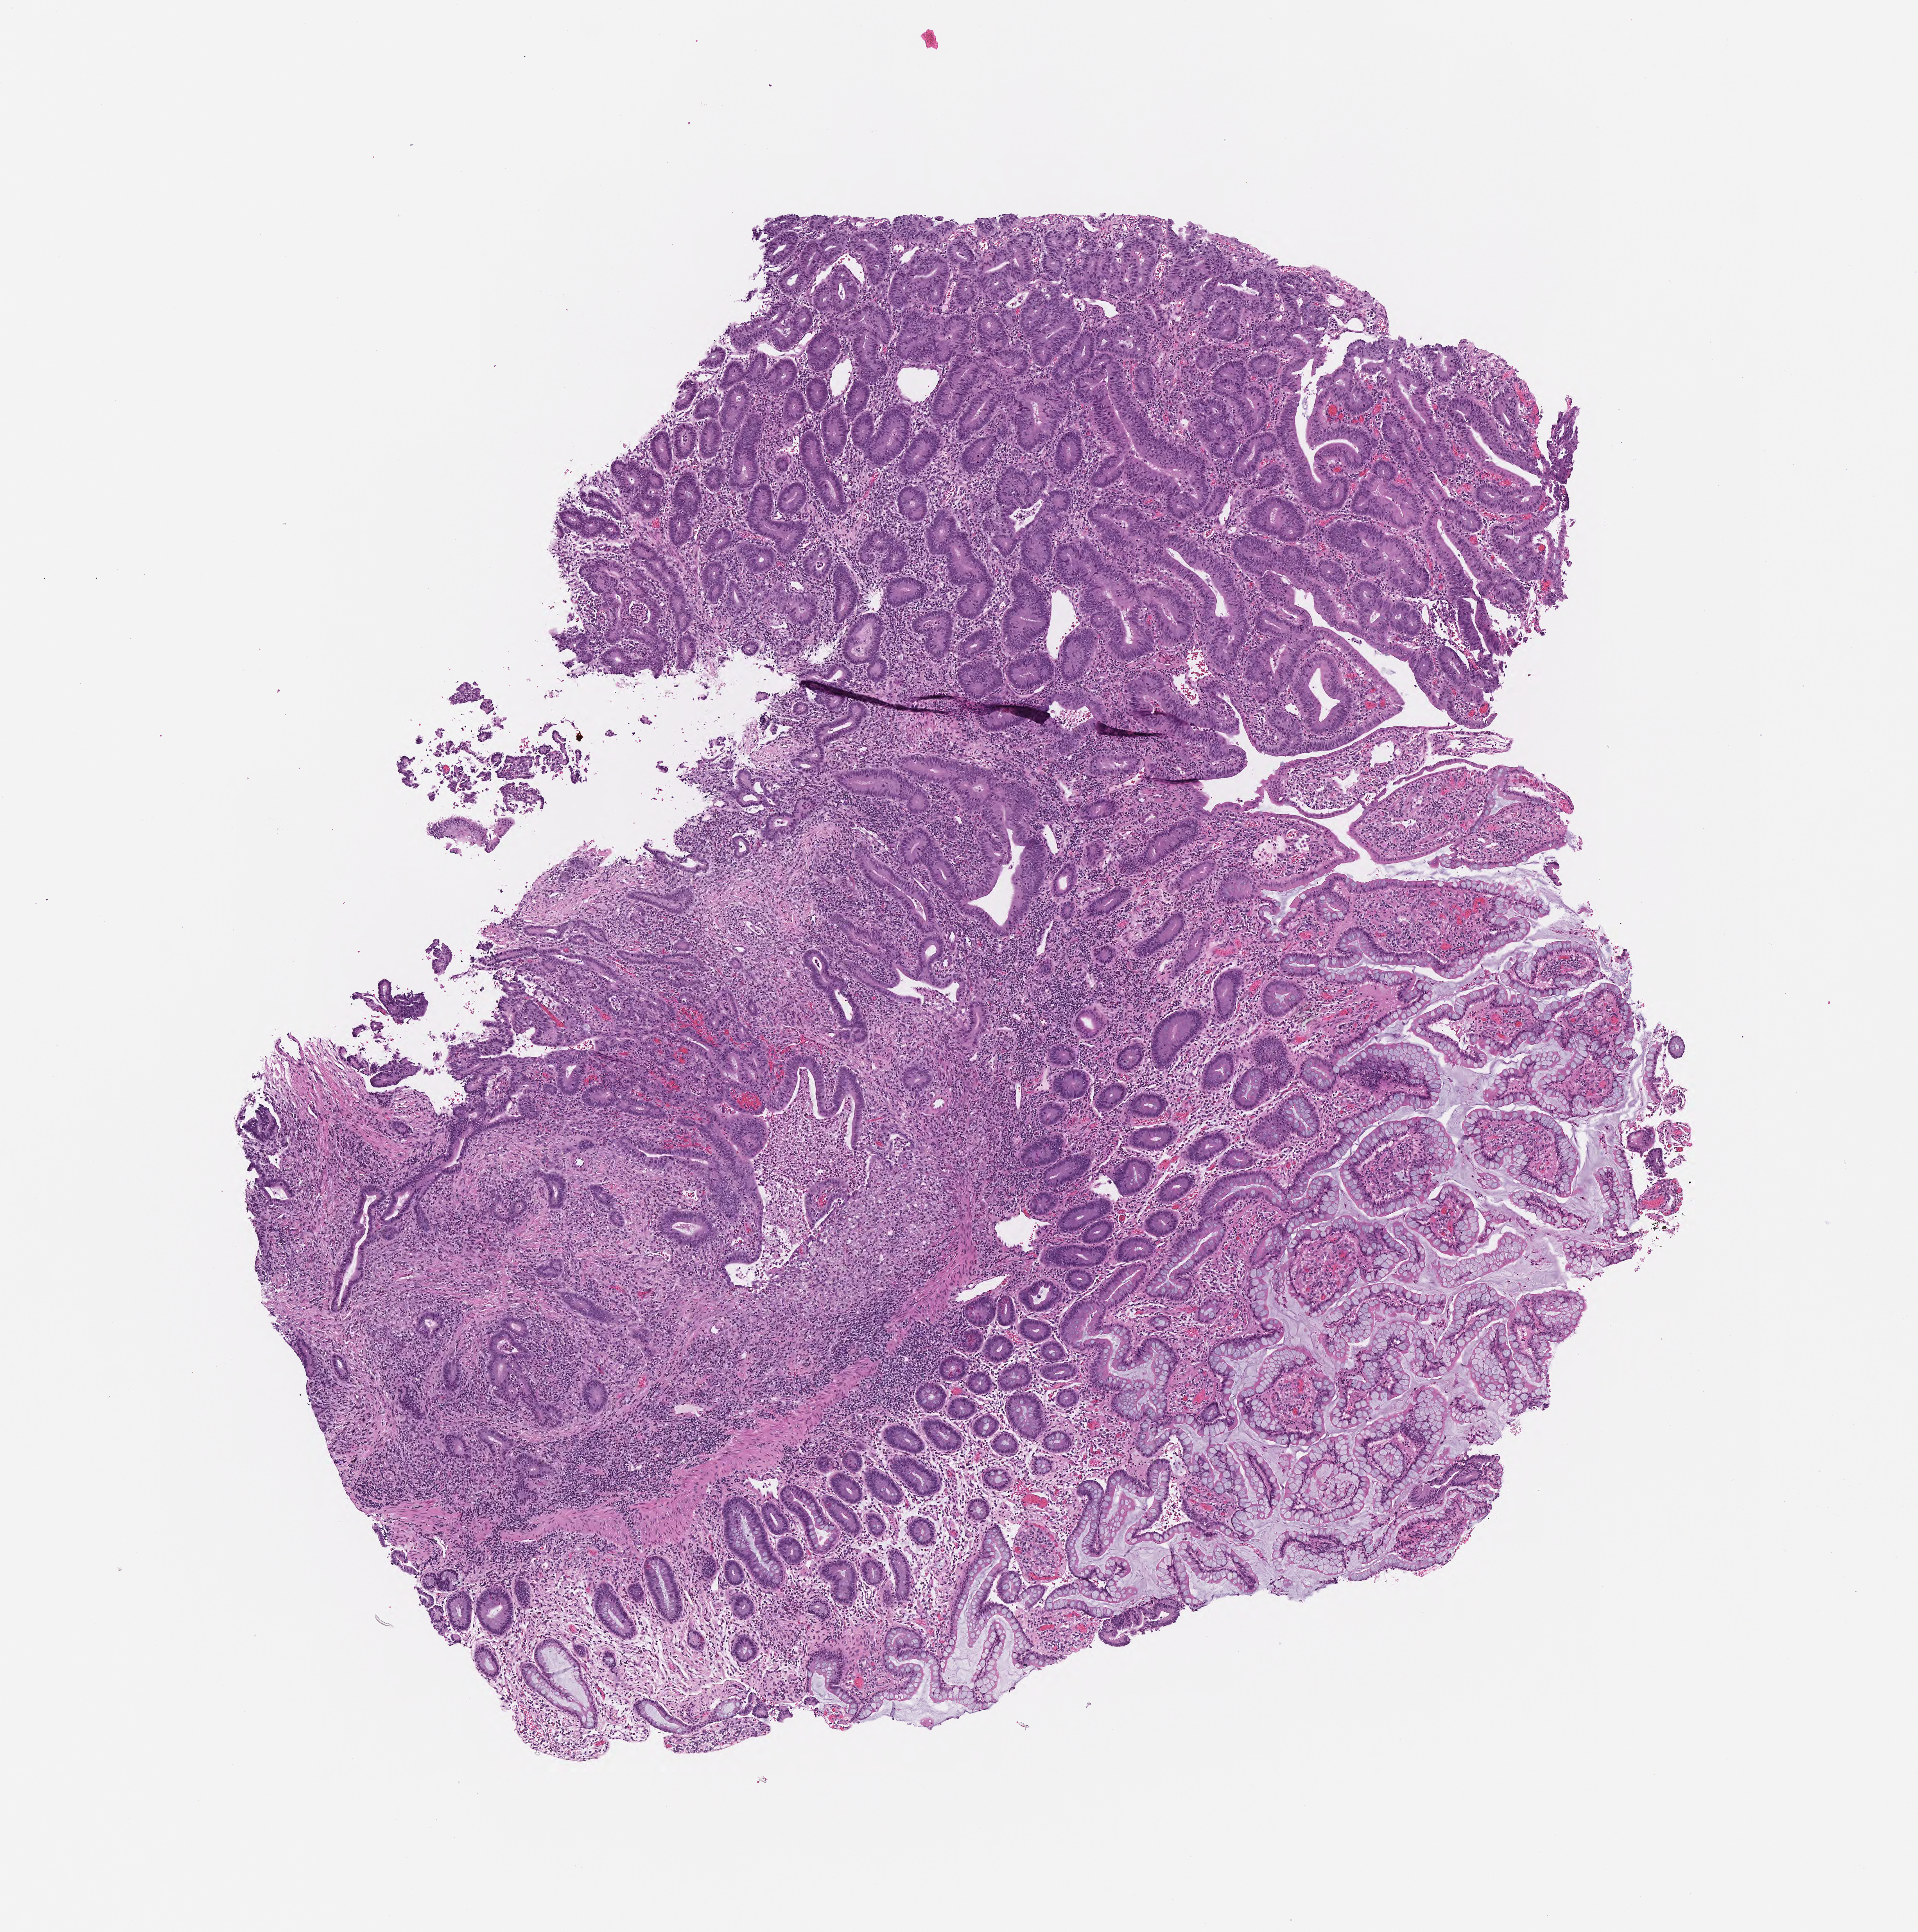
Digitized H&E-stained section — a low-resolution overview of the entire scanned area, about 6.0 x 6.1 mm; FFPE section; specimen: primary tumor; site: ileum. Male patient; age at initial diagnosis 57 years. Tumor grade: G2 (moderately differentiated). Slide review estimates, as recorded: tumor cells 65%, tumor nuclei 65%, stromal cells 28%, necrosis 2%, normal cells 5%. Infiltration values recorded for this section: lymphocyte infiltration 4%, monocyte infiltration 4%, neutrophil infiltration 14%.
* diagnosis: Adenocarcinoma, NOS
* section: top of the tissue portion
* AJCC pathologic stage: Stage I